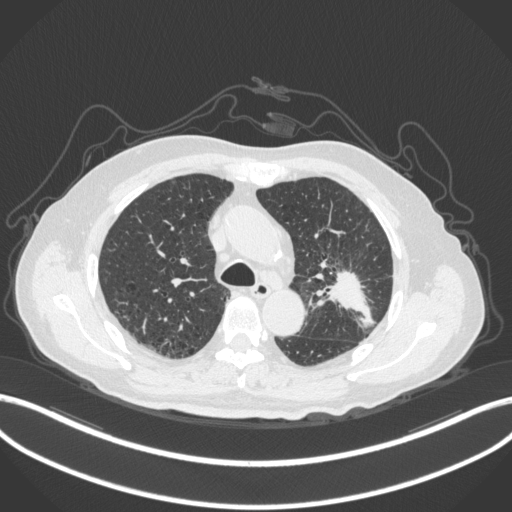
Chest CT, one axial slice; position 200 of 331 along the scan axis; lung window (W 1500 / L -600 HU); 512 × 512 image matrix, field of view 400 × 400 mm. Male patient, age 79 years. From the clinical record (not read from this slice): clinical TNM (as recorded): T2a N1 M1; histopathological grade: G3.
Annotated regions visible in this slice (rectangle marked by the reading radiologist):
- lung tumour (recorded histology: adenocarcinoma): bounding box (x1, y1, x2, y2) in pixels: (318, 265, 379, 330)